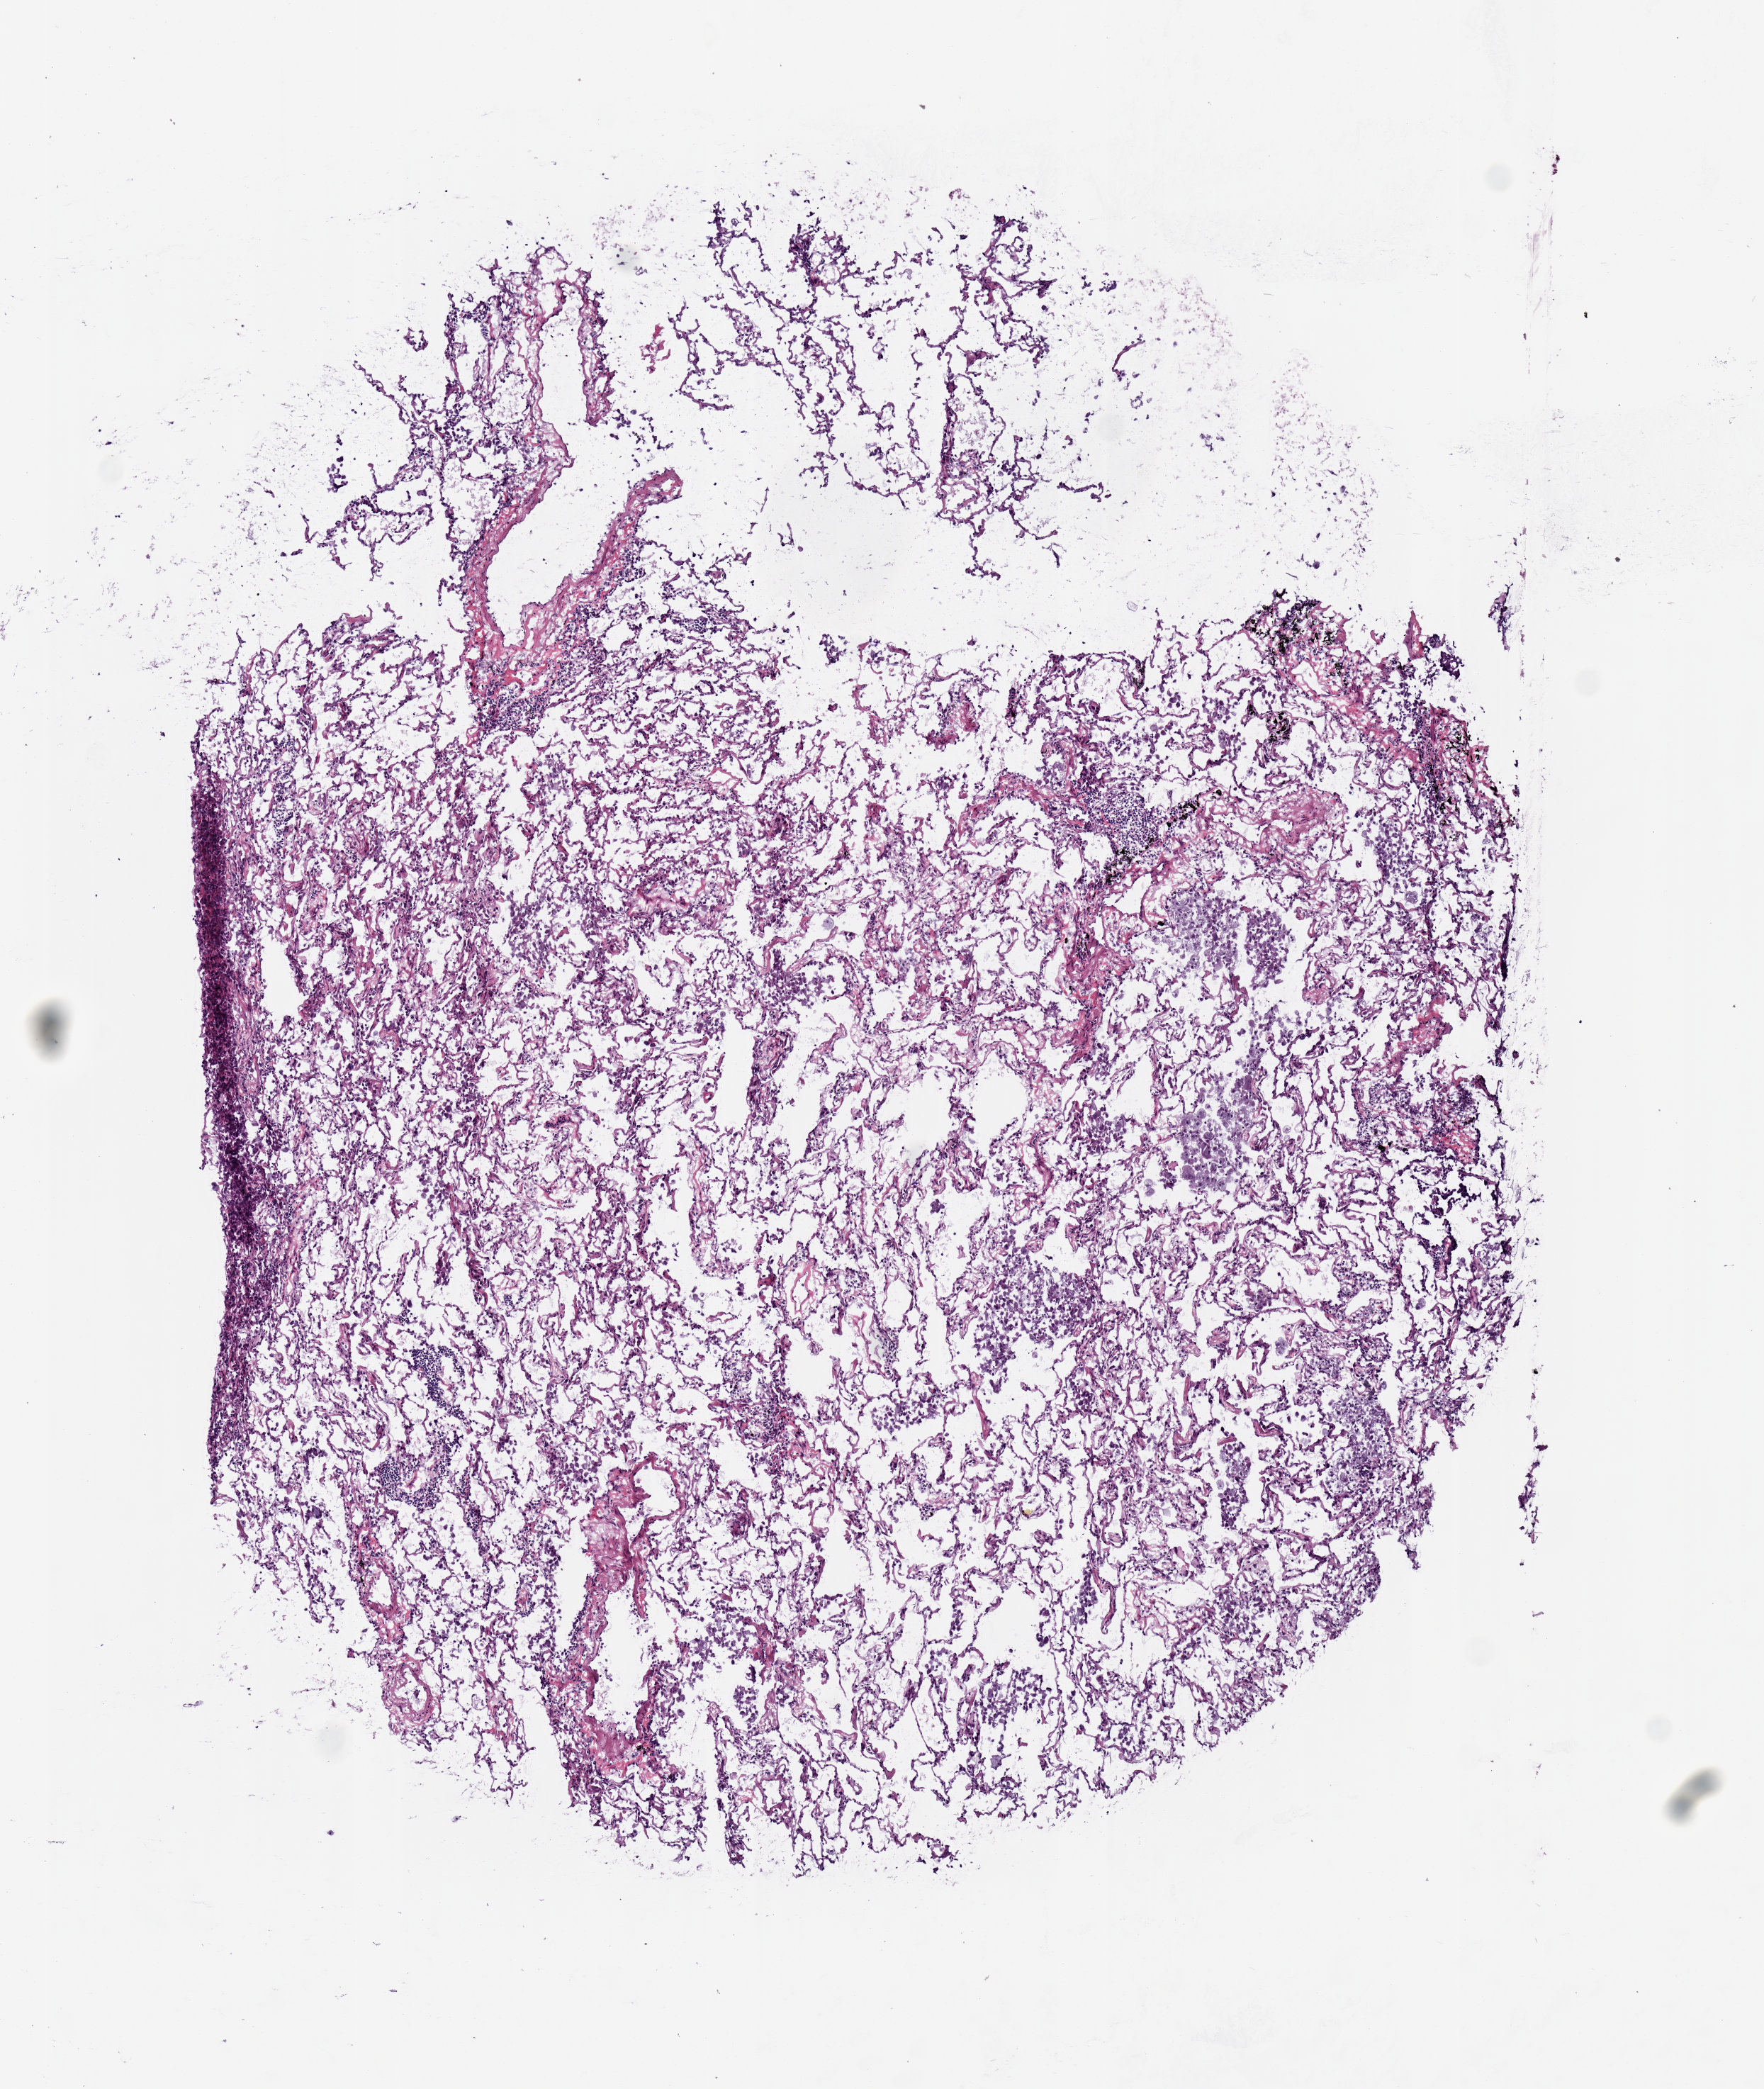
Digitized H&E-stained tissue section (whole slide), low-resolution overview of the scanned area, about 4.9 x 5.8 mm (acquisition: 20x scan). Frozen section from the top of the tissue portion. Solid tissue normal (non-tumour tissue) sample from the lung. Female patient; age at initial diagnosis 59 years.
This section: solid tissue normal sample (biorepository sample class). Patient diagnosis: Adenocarcinoma, NOS (upper lobe, lung).